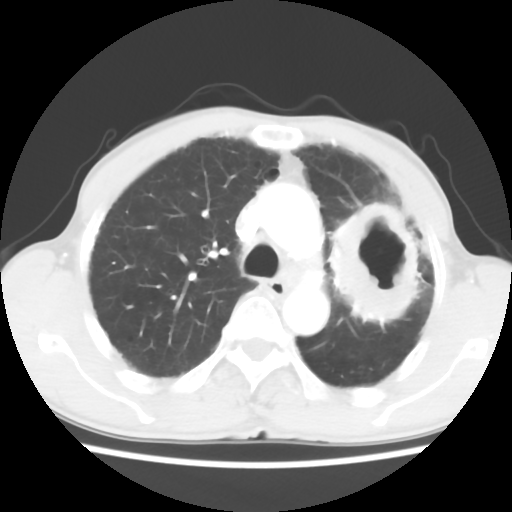
Chest CT, one axial slice. Slice 42 of 60 in the series (ordered by position). Reconstruction kernel STANDARD. Lung window (W 1500 / L -600 HU). 5 mm slice thickness. 512 × 512 image matrix. Male patient, age 64 years. Case-level facts recorded for this patient, not image findings: clinical TNM (as recorded): T3 N3 M0.
Outlined on this slice (rectangle marked by the reading radiologist):
- lung tumour (recorded histology: adenocarcinoma): bounding box [x1, y1, x2, y2] px = [319, 190, 432, 333]